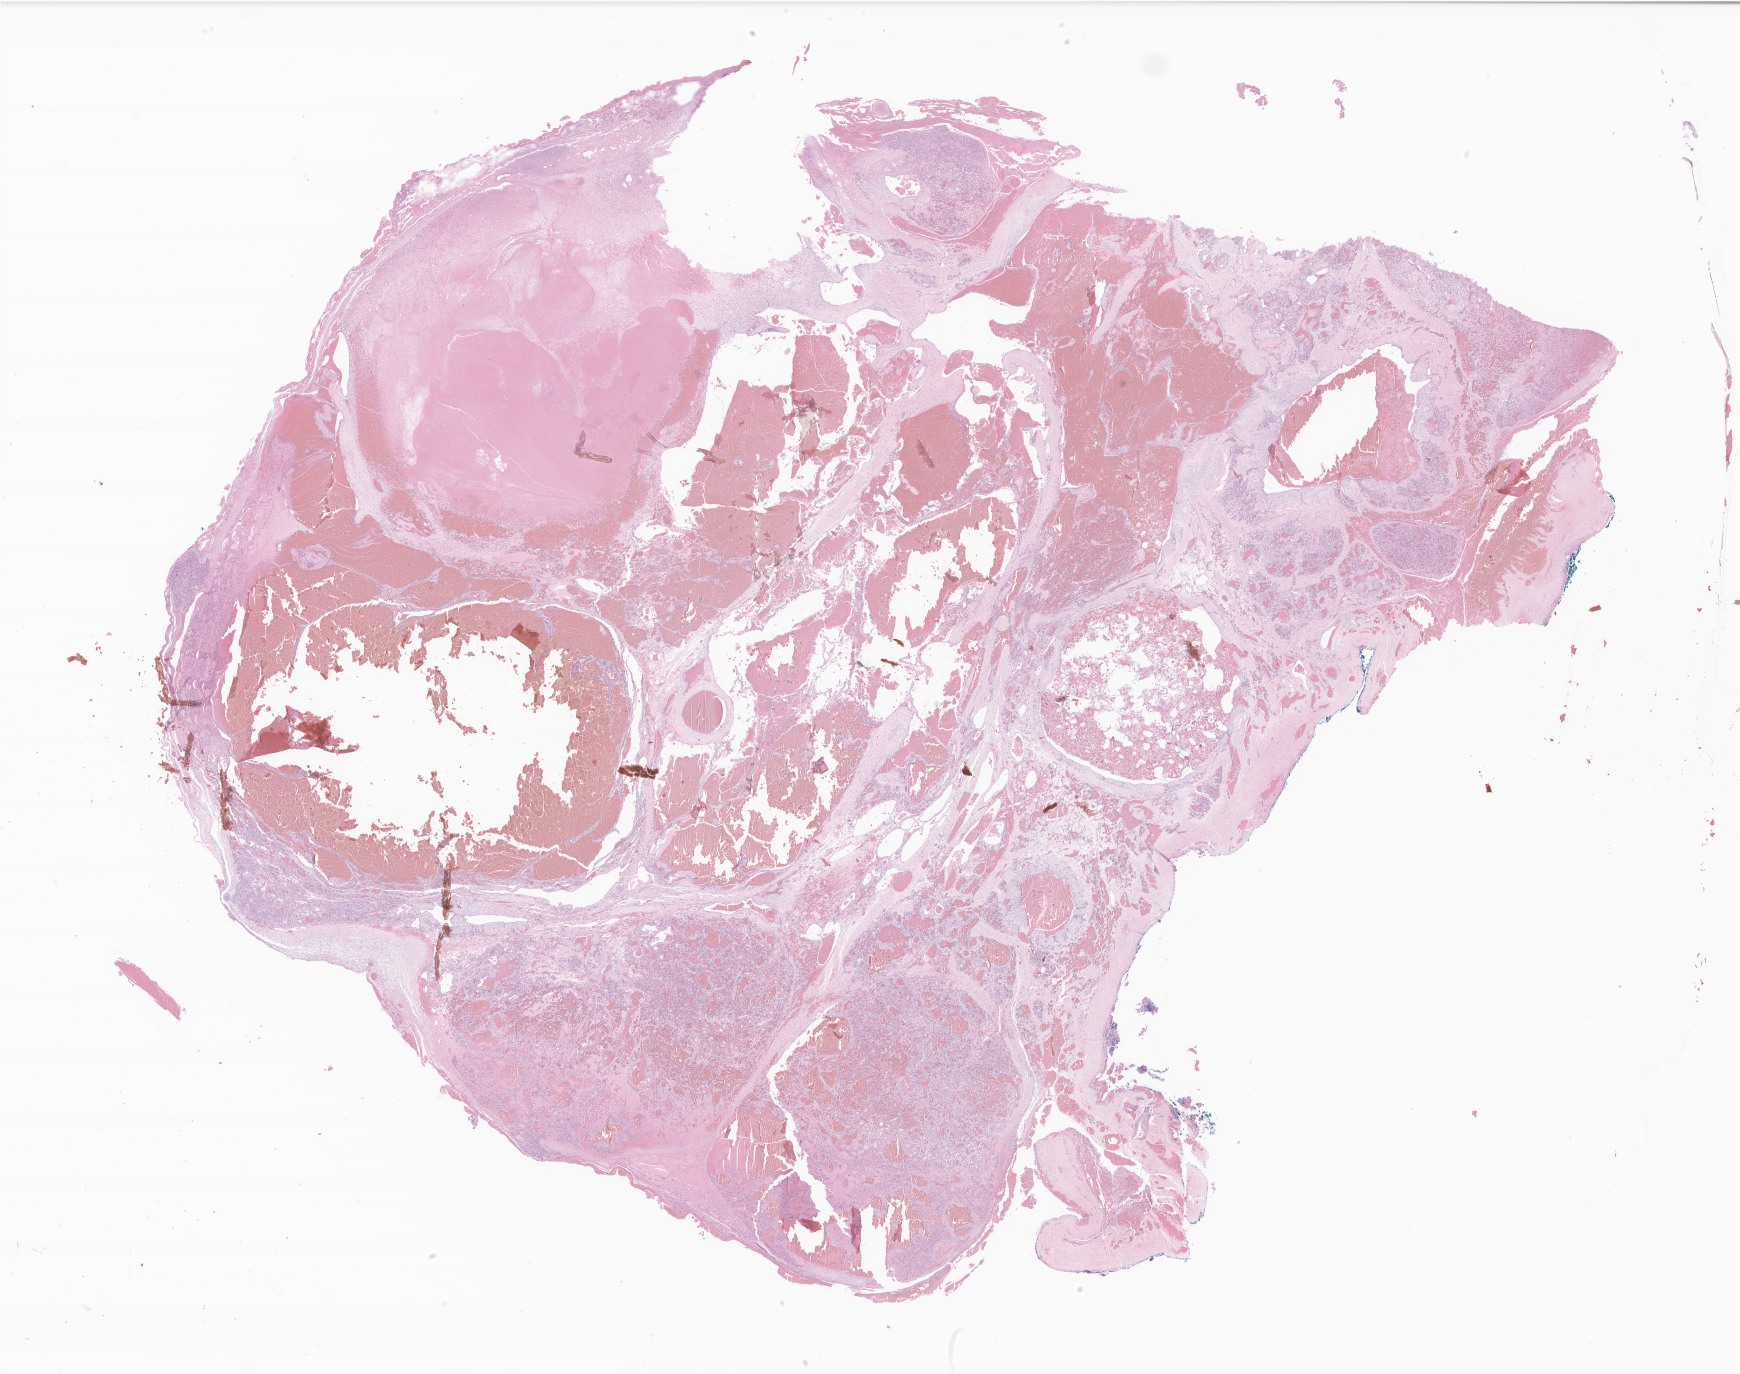
H&E whole-slide image of tumor tissue from the brain — whole scanned area (about 29.3 x 23.2 mm) shown as a low-resolution overview. Formalin-fixed, paraffin-embedded (FFPE) tissue. Patient: male, age 198 months (16 years 6 months).
- diagnosis: Hemangioma, NOS